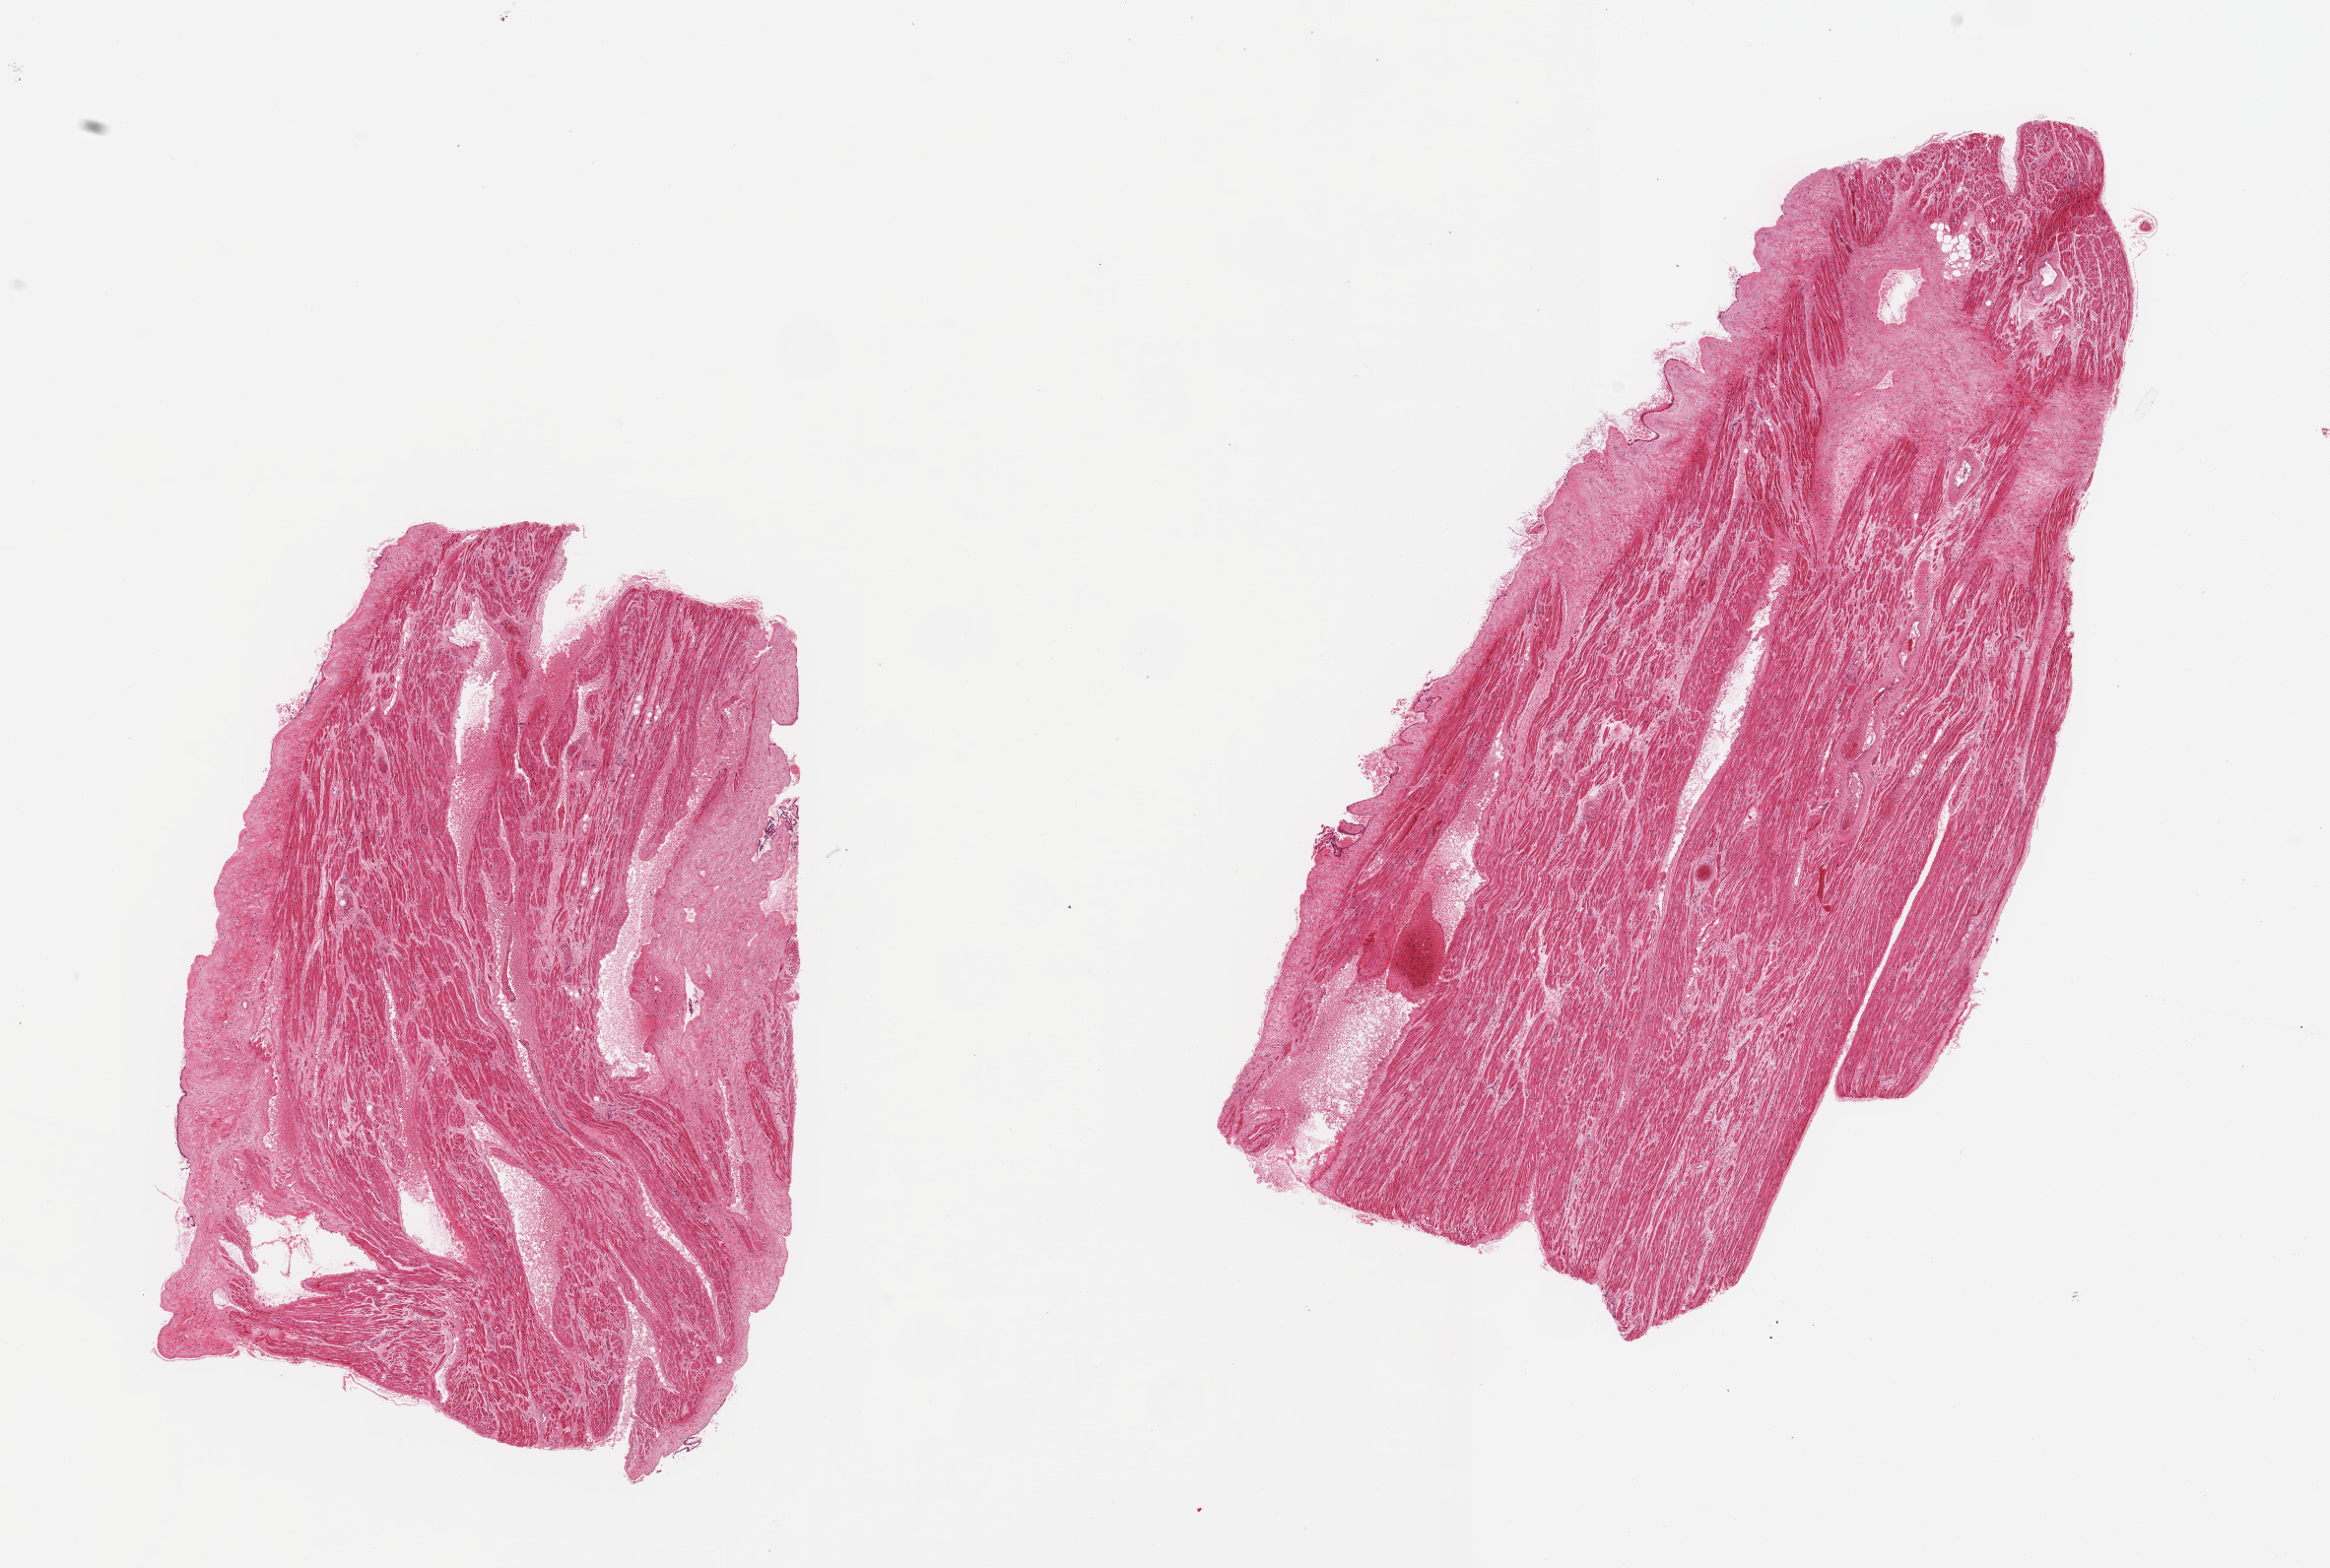
Digitized H&E-stained section, brightfield, low-resolution overview of the scanned area, about 18.7 x 12.6 mm. PAXgene-fixed, paraffin-embedded tissue. Section of auricular appendage (target tissue). Tissue donor sample.
Reviewer comment on this tissue sample: 2 pieces, no abnormalities.